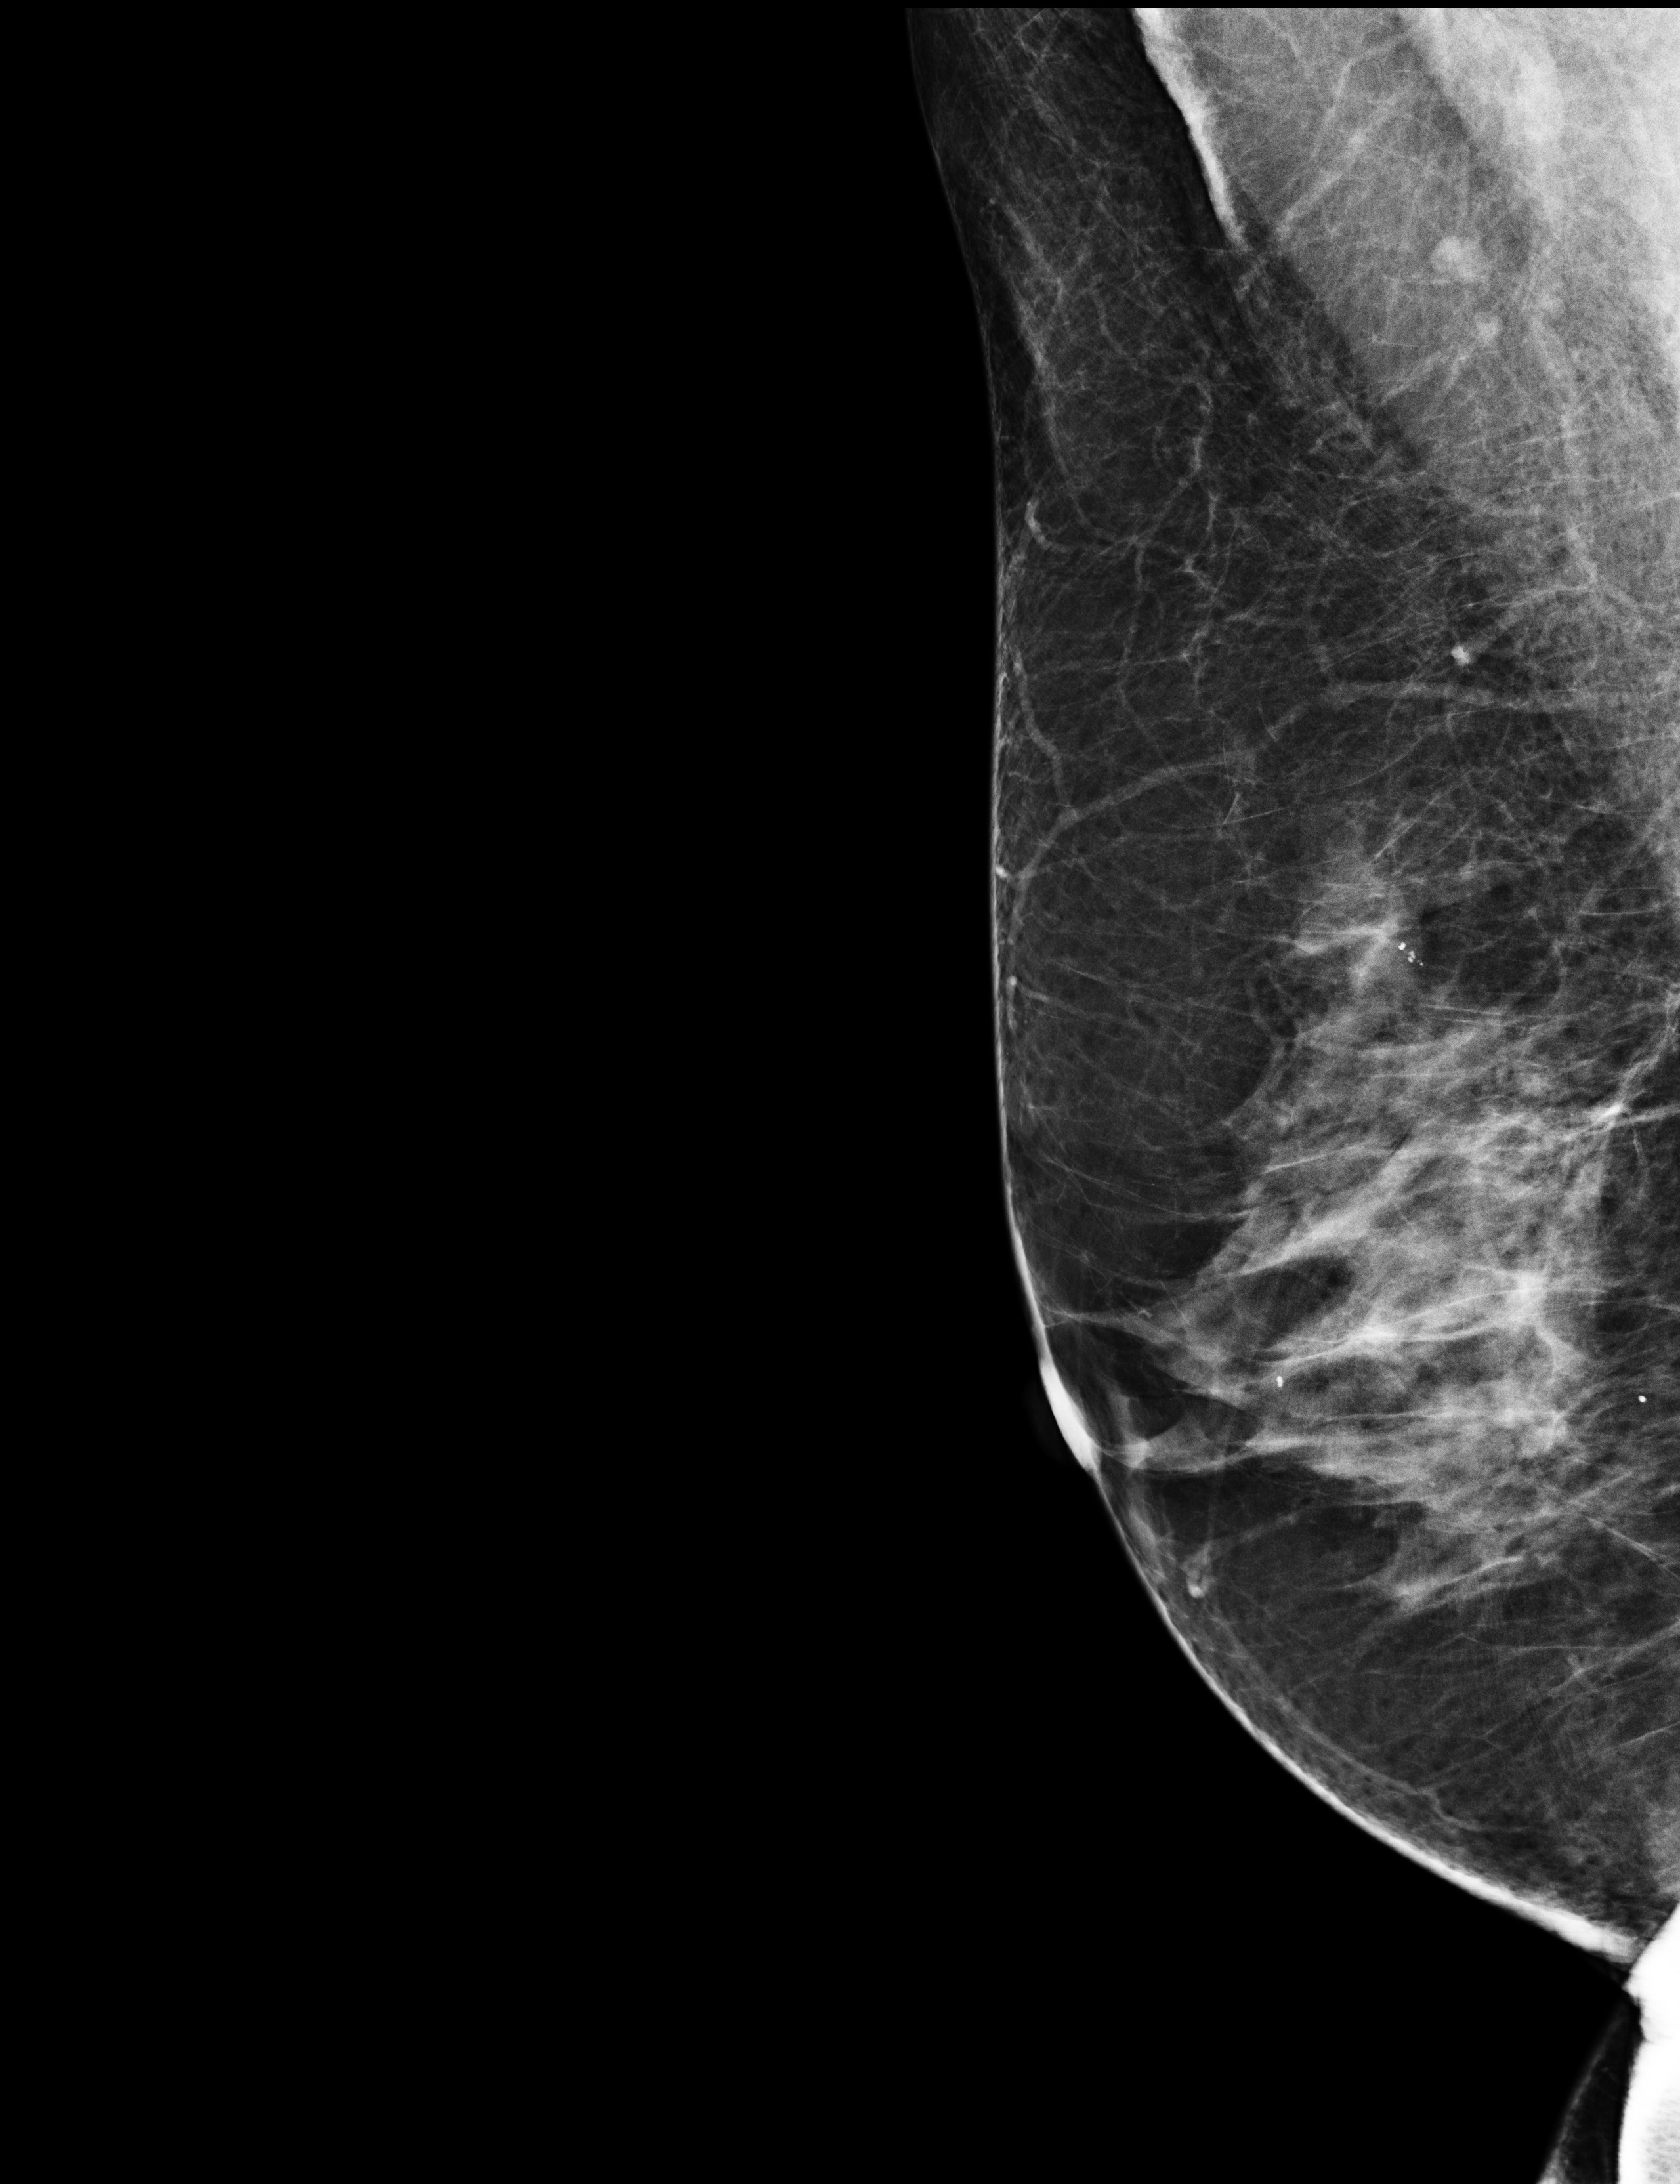
Annual screening mammography examination; compressed breast thickness 59 mm. Patient: female, 67 years.
Image type: full-field digital mammogram. Breast: right. Projection: medio-lateral oblique projection. Breast density at the screening exam (both breasts): heterogeneously dense (BI-RADS density category c). Final BI-RADS assessment for this screening round (tomosynthesis exam, both breasts): category 1. Recall: no recall after this screen.